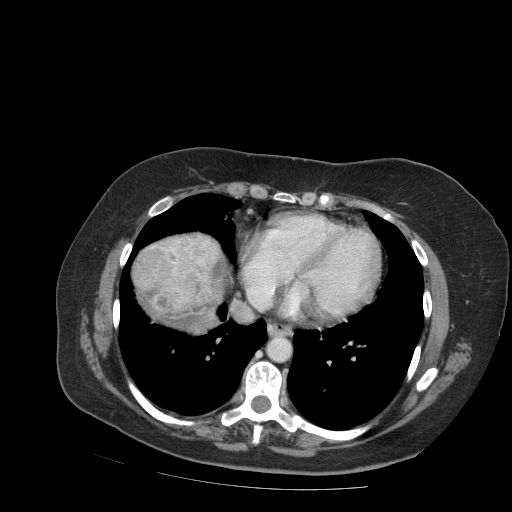
Contrast-enhanced abdominal CT (liver protocol), one axial slice; slice 88 of 99 in the series (ordered by position); reconstruction kernel STANDARD; soft-tissue window (W 400 / L 40 HU); 2.5 mm slice thickness; 512 × 512 image matrix, field of view 400 × 400 mm. From the clinical record (not read from this slice): diagnosis: hepatocellular carcinoma (patient treated with transarterial chemoembolisation; whether this scan precedes or follows treatment is not stated here); TNM stage (as recorded): Stage-IVB.
Structures marked on this image (semi-automatic segmentation, software-assisted and operator-edited):
- liver parenchyma outside the tumour (the mass and vessels are separate outlines, so this box may not span the whole liver): box from (x=132, y=234) to (x=220, y=332) px
- mass: (x=137, y=244)–(x=230, y=328)